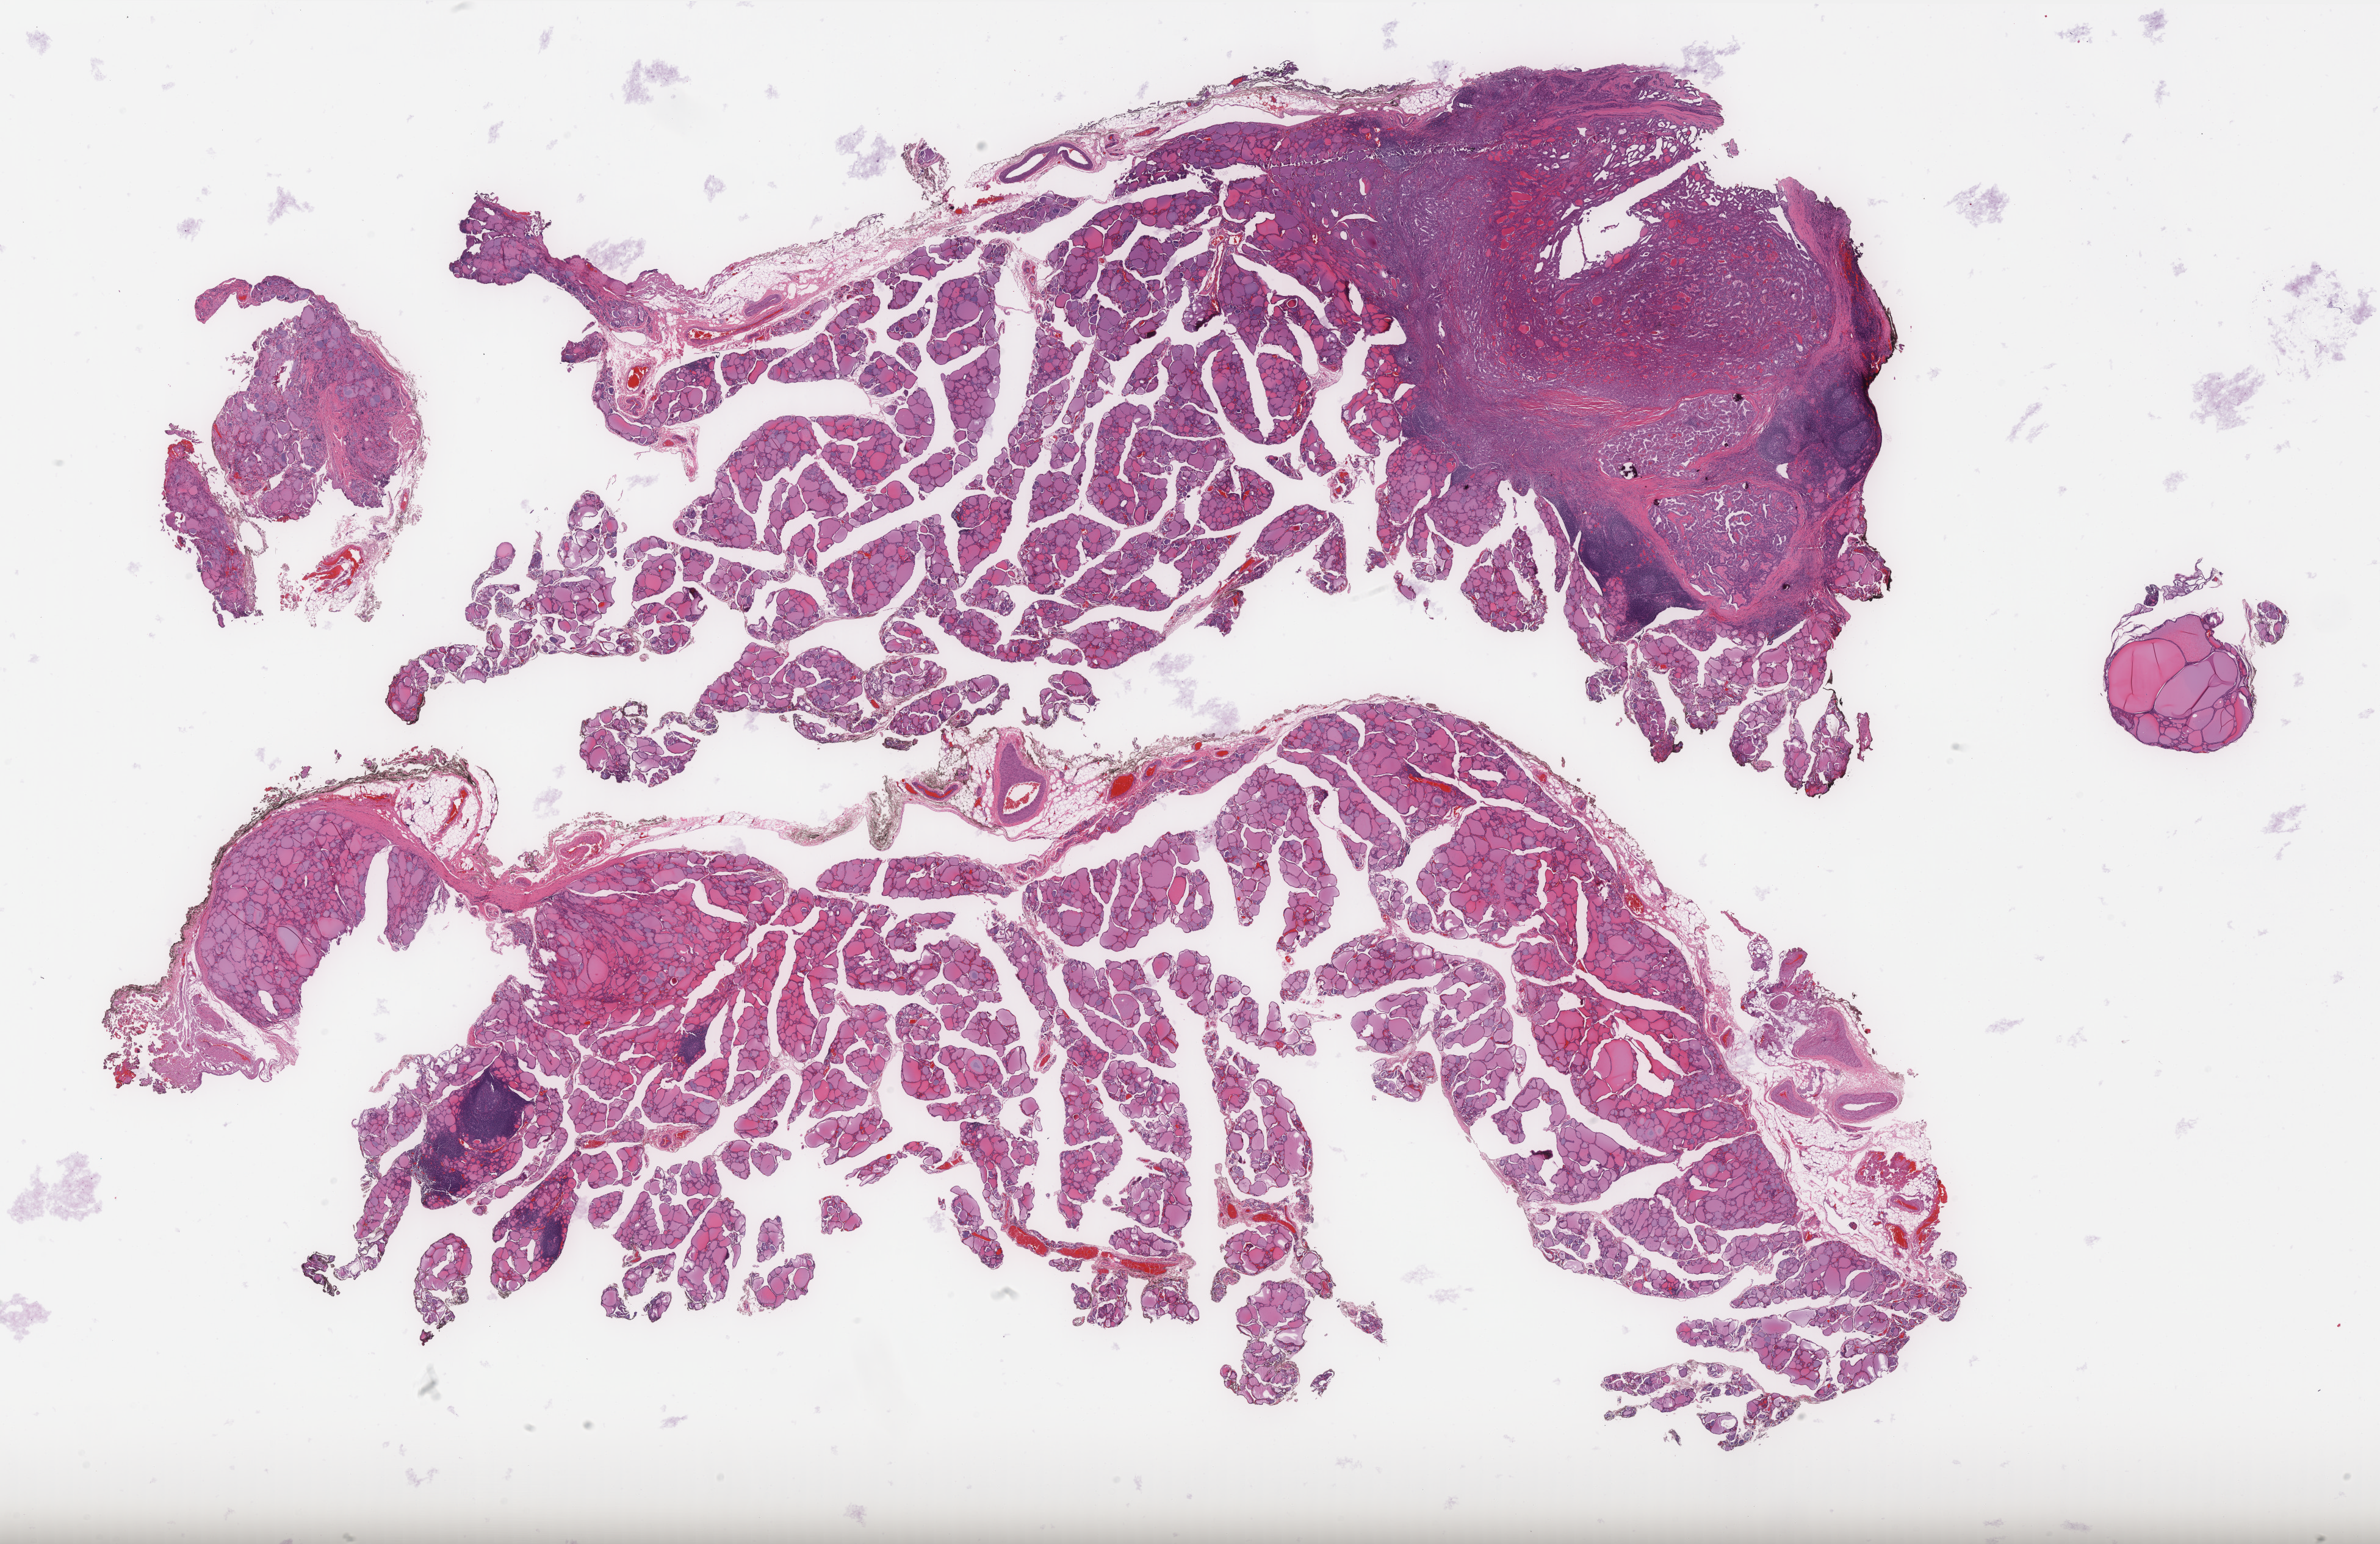
Whole-slide histology image, H&E-stained, low-resolution overview of the scanned area, about 31.3 x 20.3 mm, formalin-fixed paraffin-embedded (FFPE) diagnostic section, sample: primary tumour, thyroid. Patient: male, age at initial diagnosis 43 years.
Diagnosis: Papillary adenocarcinoma, NOS (thyroid gland). TNM: T3 N0 M0. AJCC pathologic stage: I (7th edition).